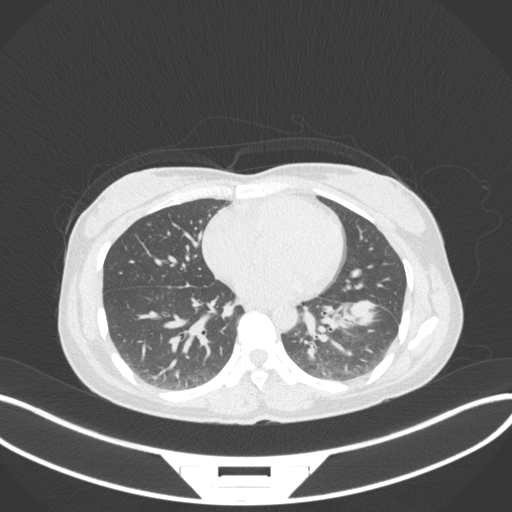
Chest CT, one axial slice; position 150 of 361 along the scan axis; 120 kVp; lung window (W 1500 / L -600 HU); 1 mm slice thickness; 512 × 512 image matrix, field of view 400 × 400 mm. Female patient, age 41 years. Case-level facts recorded for this patient, not image findings: clinical TNM (as recorded): T2a N3 M1b.
Outlined on this slice (bounding box drawn by a radiologist):
- lung tumour (recorded histology: adenocarcinoma): bounding box <337,296,389,335> (left, top, right, bottom; pixels)